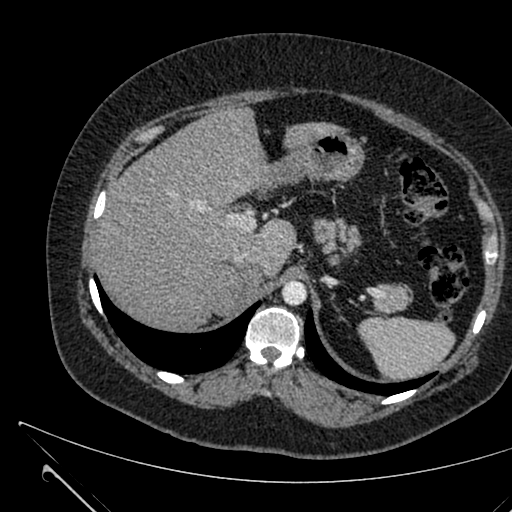
Contrast-enhanced abdominal CT, one axial slice; position 479 of 731 along the scan axis; soft-tissue window (W 400 / L 40 HU); 512 × 512 image matrix, field of view 376 × 376 mm. Patient: female, 36 years. Case-level facts recorded for this patient, not image findings: diagnosis: adrenocortical carcinoma; tumour side: right adrenal; tumour size at pathology: 10 cm; Ki-67 index: 20 %; stage (as recorded): 4.
Annotated regions visible in this slice (semi-automatically segmented with operator editing):
- mass: bounding box <217,268,260,314> (left, top, right, bottom; pixels)